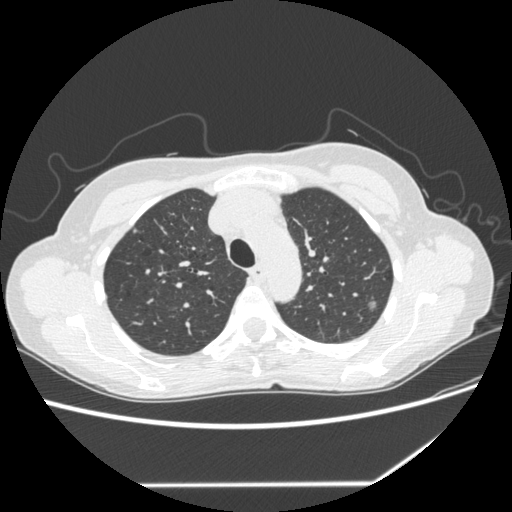
Low-dose screening chest CT, one axial slice; position 200 of 255 along the scan axis; reconstruction kernel STANDARD; lung window (W 1500 / L -600 HU); 1.25 mm slice thickness; 512 × 512 image matrix, field of view 360 × 360 mm.
Outlined on this slice (manually delineated by an expert):
- lesion 1 (tumor, upper lobe of left lung): bounding box [x1, y1, x2, y2] px = [369, 301, 376, 309]